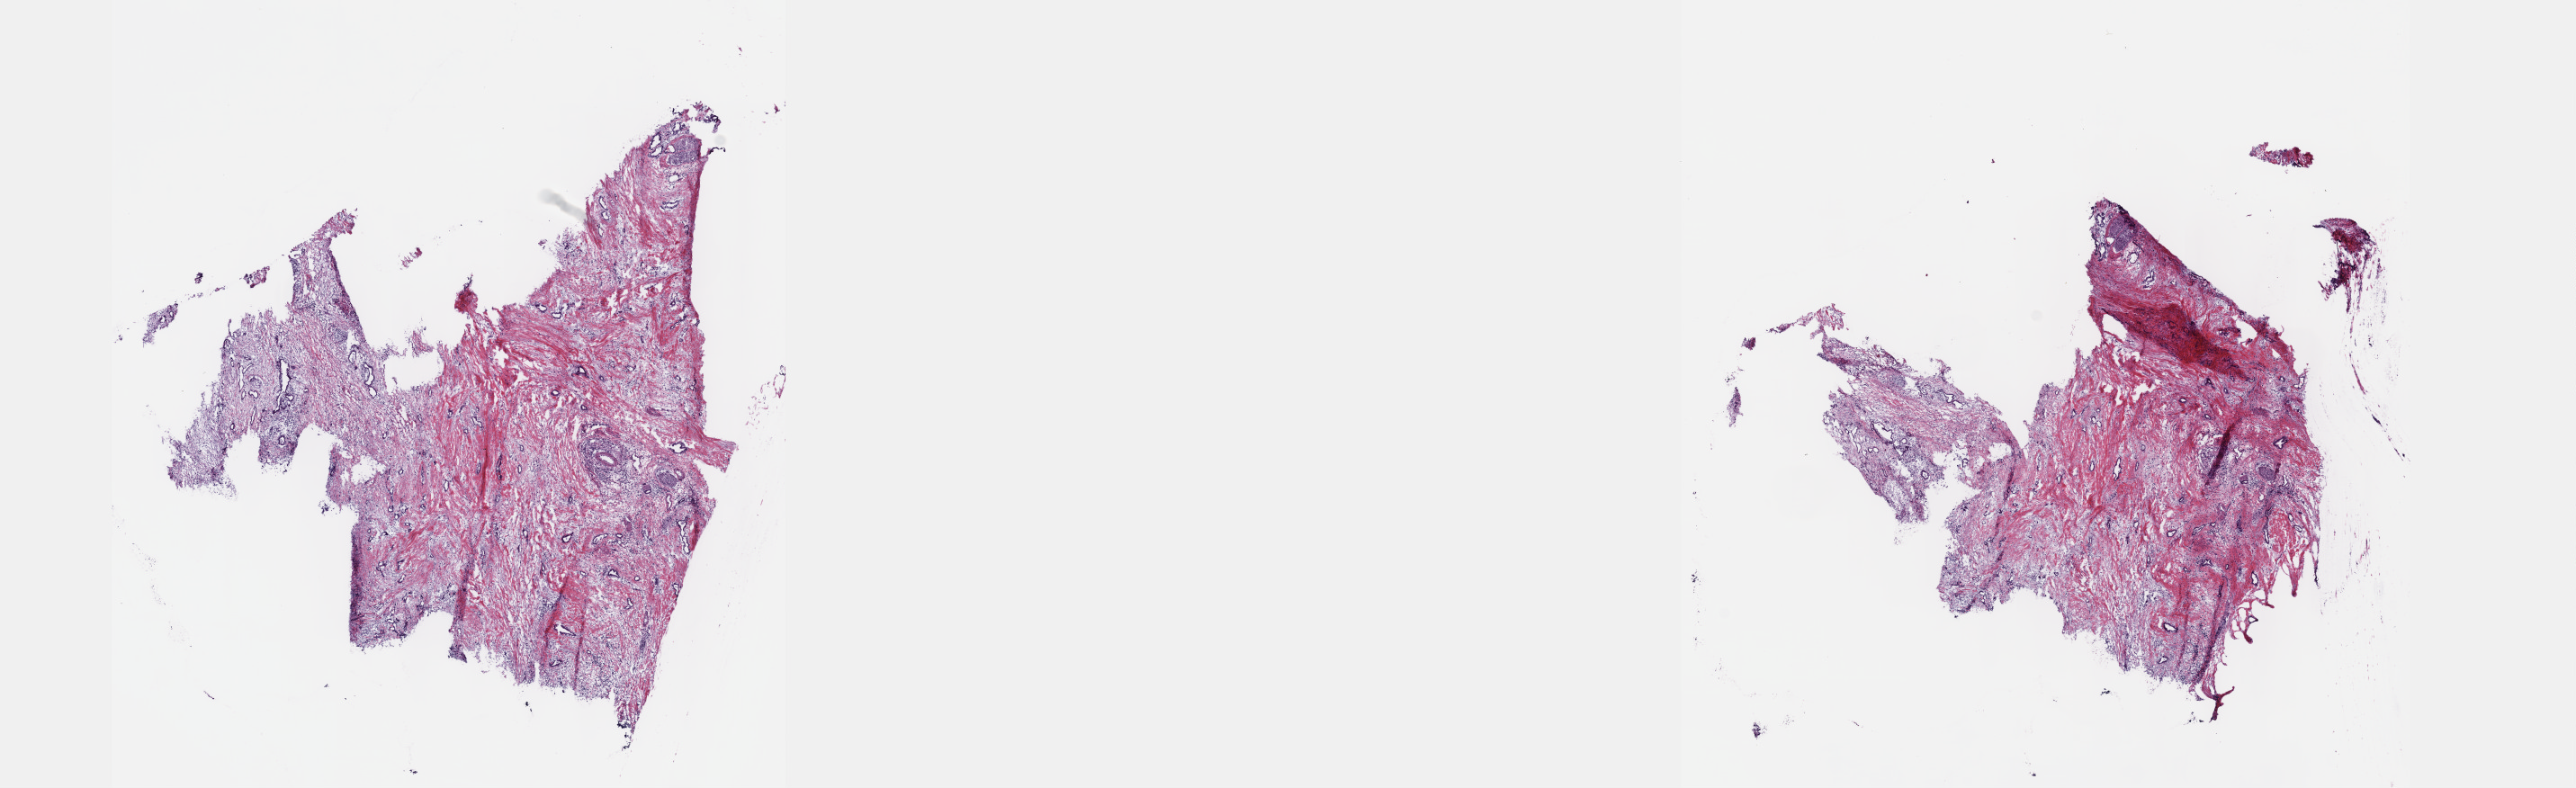
Whole-slide histology image, H&E-stained — low-resolution overview of the scanned area, about 23.1 x 7.1 mm, frozen section from the top of the tissue portion, sample: primary tumour, pancreas. Male, age 55 years at initial diagnosis. Histologic grade: G2 (moderately differentiated). Pathologist review of this section (percent, as recorded): tumour cells 70%, tumour nuclei 70%, normal cells 0%, stromal cells 30%, necrosis 0%. Inflammatory infiltration, as recorded: lymphocyte infiltration 40%, monocyte infiltration 20%, neutrophil infiltration 20%.
AJCC pathologic stage: IIB (7th edition). Histologic diagnosis: Infiltrating duct carcinoma, NOS (head of pancreas). TNM: T3 N1 M0. Lymph nodes positive (case pathology): 2 of 22 examined.